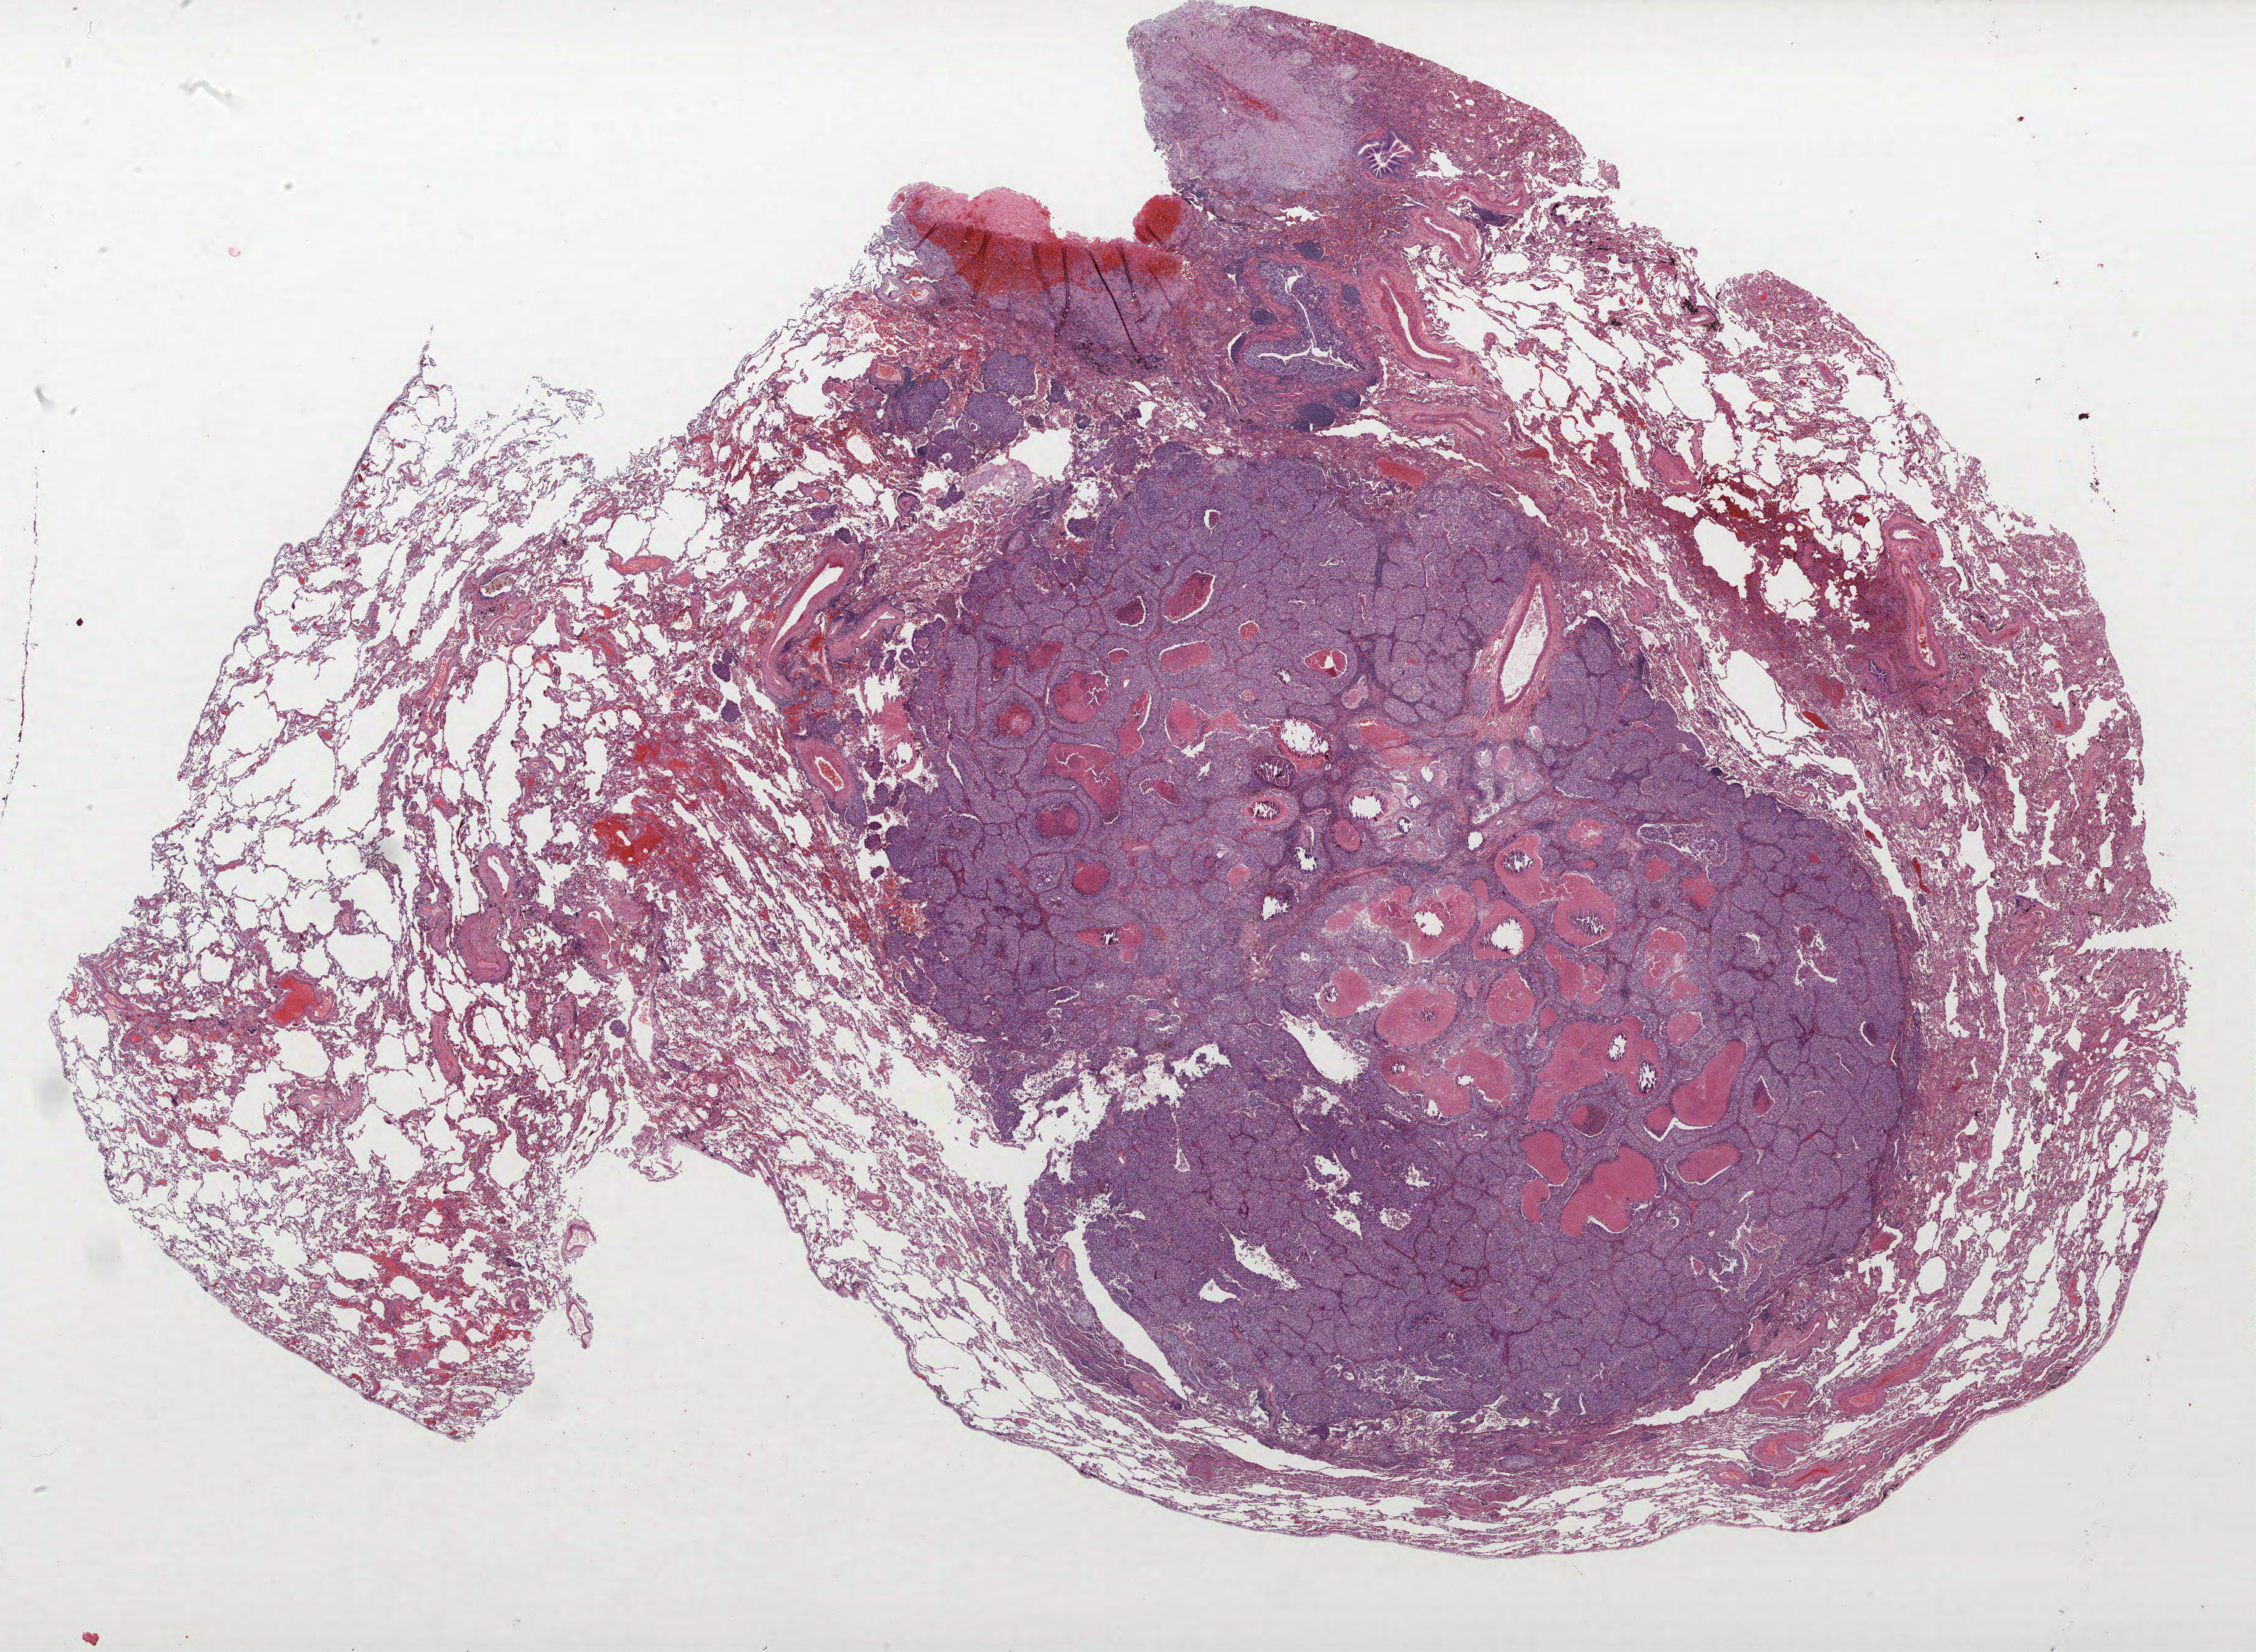
Whole-slide histology image, Hematoxylin and eosin (H&E) stained, shown as a low-resolution overview of the whole scanned area (about 29.3 x 21.4 mm), formalin-fixed paraffin-embedded (FFPE) section, lung tissue. Female, age 59 at enrolment. Current smoker at enrolment. Grade: poorly differentiated (G3).
Participant's lung-cancer diagnosis: Non-small cell carcinoma. Primary tumour location (clinical record): right lower lobe. Stage (AJCC 6th edition): IA. Tumour size (pathology): 15 mm.